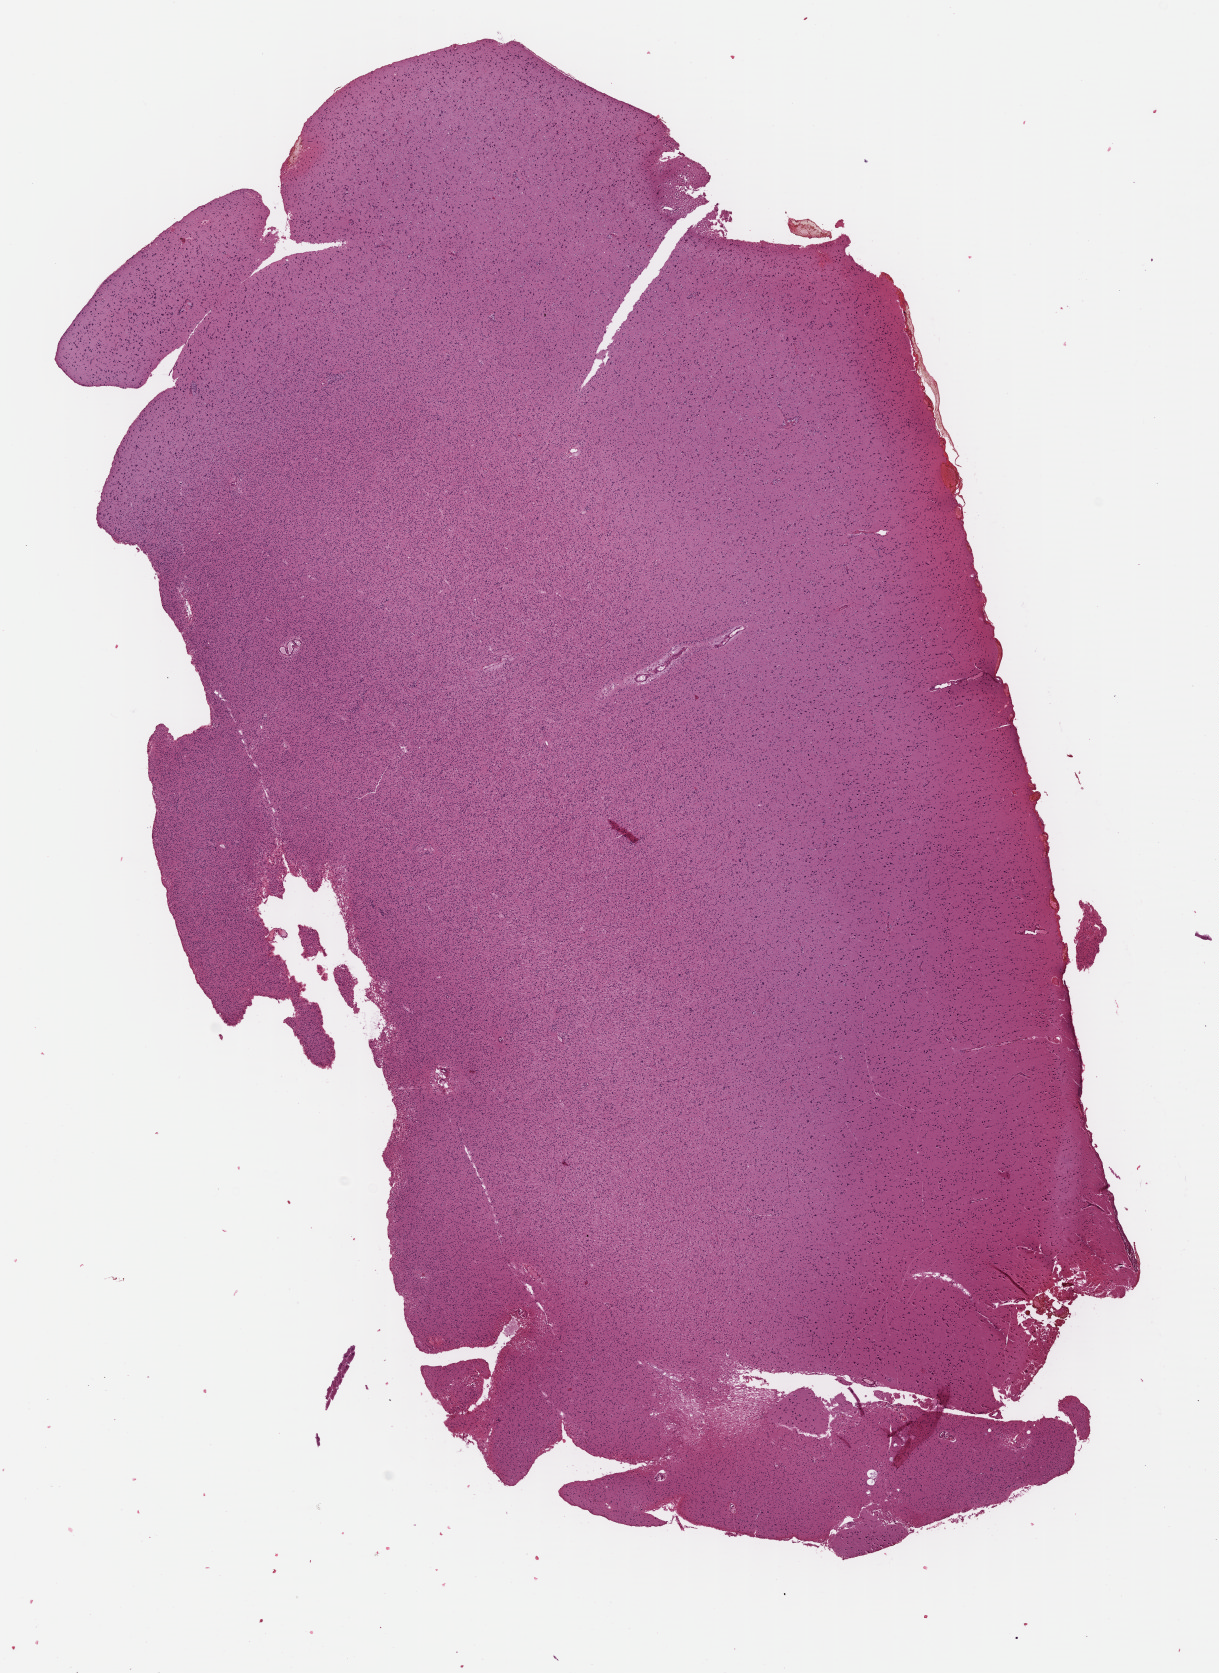
Whole-slide histology image, Hematoxylin and eosin (H&E) stained, a low-resolution overview of the entire scanned area, about 9.6 x 13.2 mm (slide scanned at 40x); formalin-fixed paraffin-embedded (FFPE) diagnostic section; brain, primary tumour sample. Female patient; age at initial diagnosis 20 years. Histologic grade: G2 (moderately differentiated).
* laterality: left
* histologic diagnosis: Oligodendroglioma, NOS